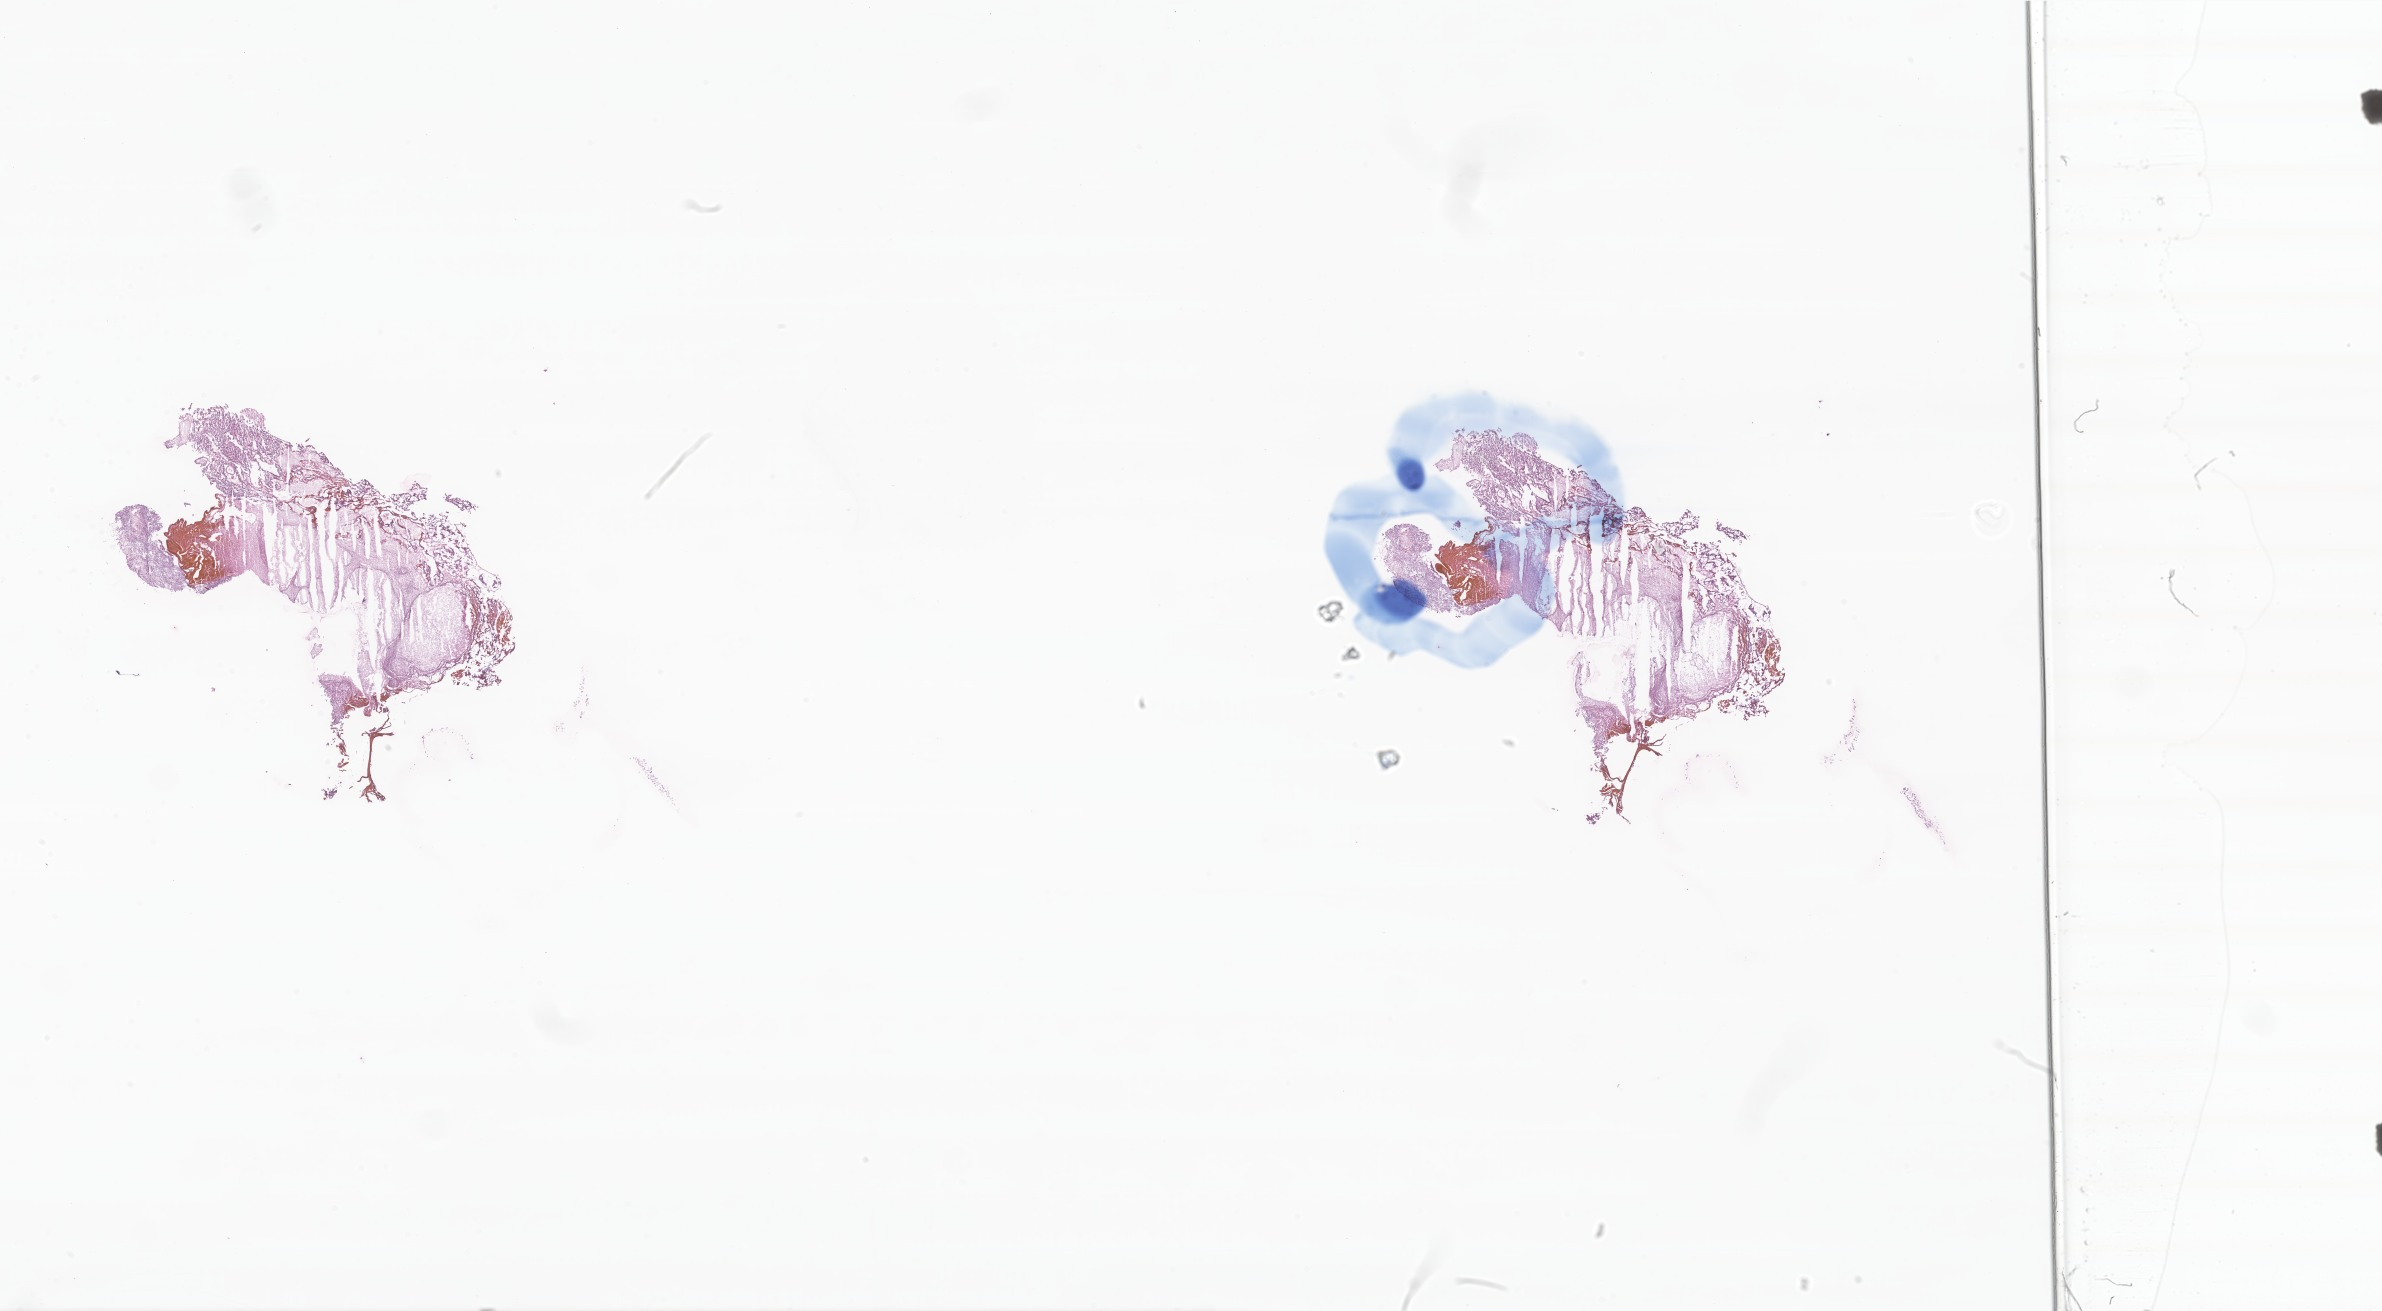
Whole-slide image, hematoxylin and eosin (H&E) stain of tumor tissue from the brain — low-resolution overview of the scanned area, about 40.2 x 22.1 mm; cryosection (OCT / tissue freezing medium). Patient male; age 97 months (8 years 1 month).
Diagnosis: Ependymoma, NOS.